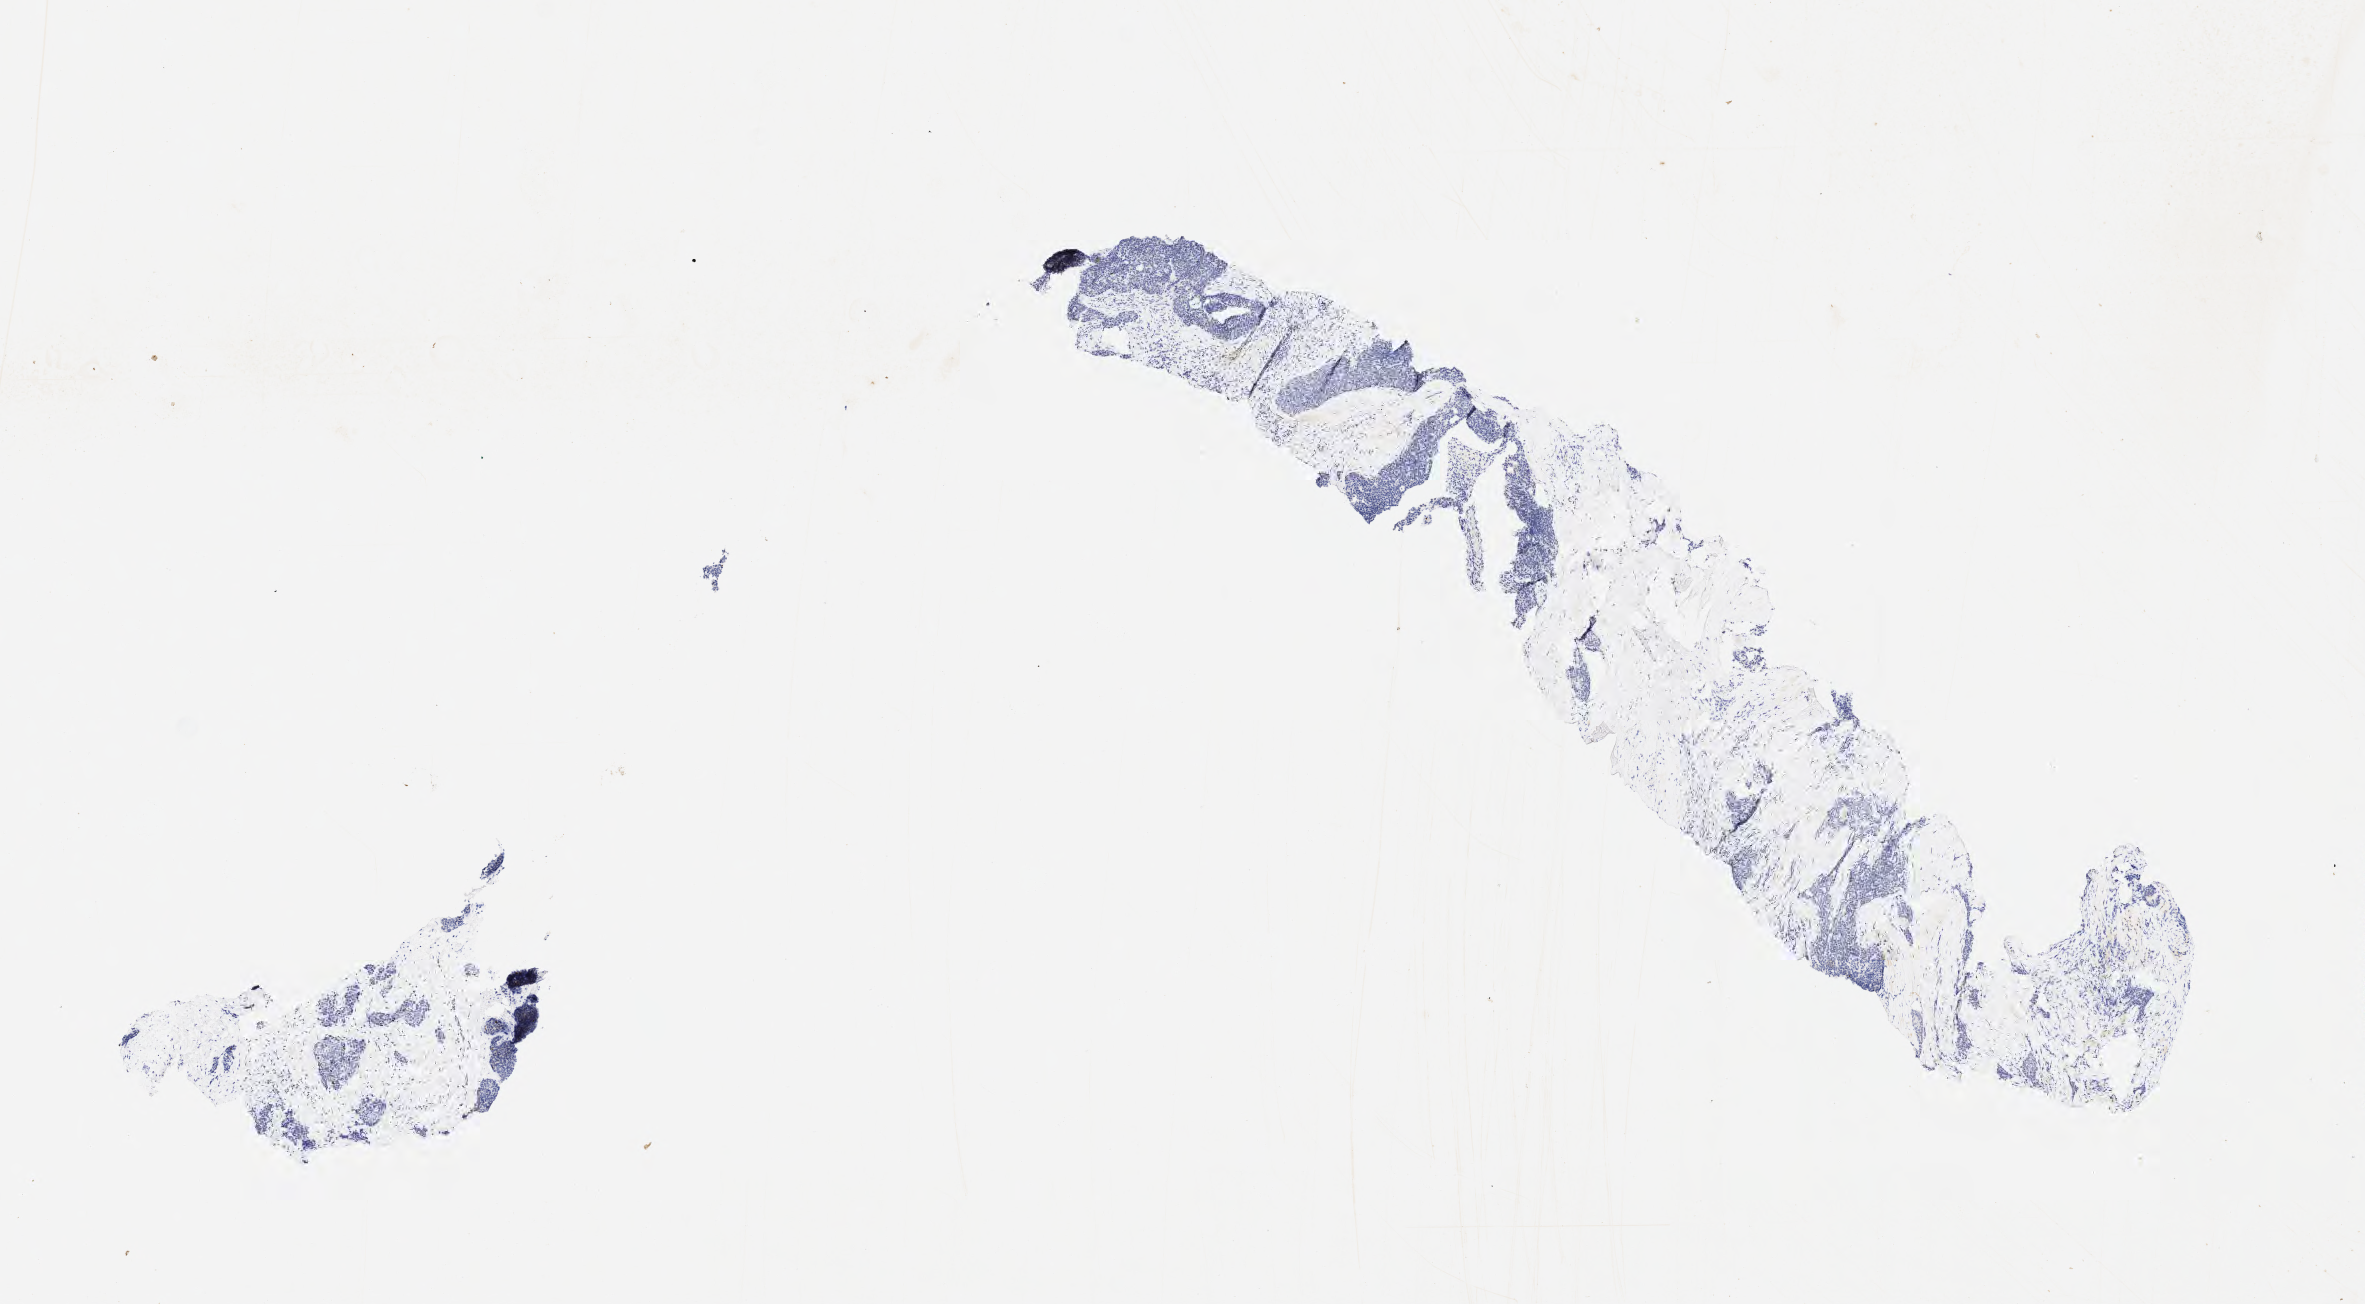
Immunohistochemistry (IHC) whole-slide image stained for TTF-1 (thyroid transcription factor 1) — a low-resolution overview of the entire scanned area, about 9.6 x 5.3 mm. Tumor tissue. Site: lung. Patient female; 68 years old.
Histologic diagnosis: Squamous cell carcinoma, large cell, nonkeratinizing, NOS.